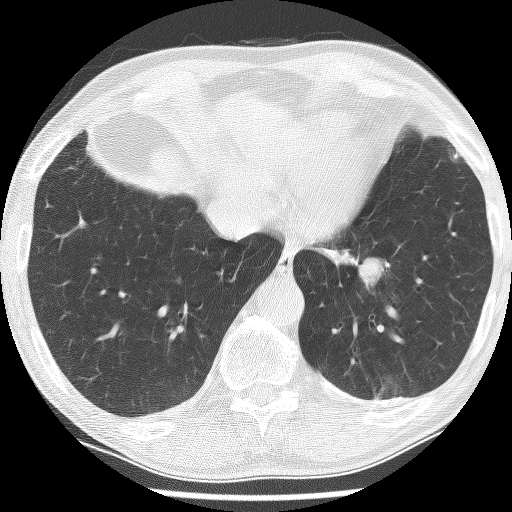
Axial slice from a low-dose chest CT screening exam, first (baseline) screen, lung window (W 1500 / L -600 HU), 2.5 mm slice thickness, 512 × 512 image matrix, field of view 320 × 320 mm. Male, age 74 years at enrolment. Current smoker at enrolment.
Expert reader's lesion annotation, bounding box (x1, y1, x2, y2) in pixels: (311, 213, 410, 305). Reader record for this screening exam (exam-level; its link to the box is not recorded): non-calcified nodule or mass ≥4 mm, left lower lobe, 30 × 27 mm, spiculated (stellate) margins, soft tissue attenuation. Participant outcome: lung cancer diagnosed 151 days after this screen — adenocarcinoma, NOS, left lower lobe, stage IIIA (AJCC 6th edition), 49 mm at pathology.